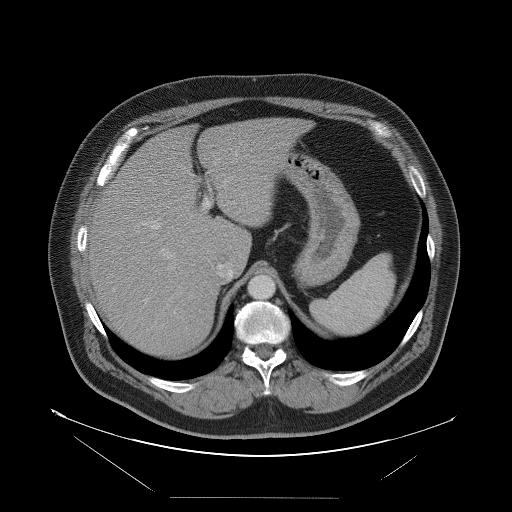
Contrast-enhanced abdominal CT, one axial slice; position 71 of 114 along the scan axis; intravenous contrast given; soft-tissue window (W 400 / L 40 HU); 5 mm slice thickness; 512 × 512 image matrix, field of view 500 × 500 mm. Male patient, age 61 years. From the clinical record (not read from this slice): diagnosis: colorectal cancer liver metastases, imaged before liver resection; multiple liver metastases: no; largest metastasis: 6.5 cm; disease in both lobes: yes.
Outlined on this slice (manually delineated by an expert):
- hepatic veins: bounding box <149,177,234,280> (left, top, right, bottom; pixels)
- liver: <89,118,304,355>
- planned liver remnant (the part of the liver to remain after resection): <145,118,304,266>
- portal vein (with intrahepatic branches): <141,151,238,302>